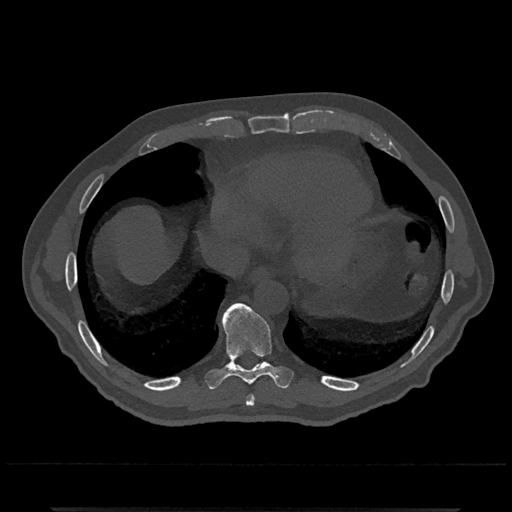
CT including the spine, one axial slice. Position 612 of 797 along the scan axis. 120 kVp. Bone window (W 1800 / L 400 HU). 0.5 mm slice thickness. 512 × 512 image matrix. Patient: male, 67 years. From the clinical record (not read from this slice): primary cancer: prostate.
Annotated regions visible in this slice (semi-automatic segmentation, software-assisted and operator-edited):
- T8 vertebra: bounding box (x1, y1, x2, y2) in pixels: (246, 395, 255, 406)
- T9 vertebra: (205, 303, 294, 389)